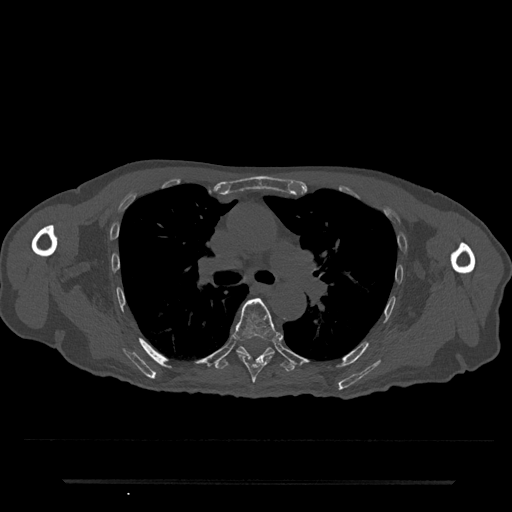
CT including the spine, one axial slice; position 513 of 797 along the scan axis; reconstruction kernel Br40s/3; 120 kVp; bone window (W 1800 / L 400 HU); 0.5 mm slice thickness; 512 × 512 image matrix. Patient: male, 74 years. Case-level facts recorded for this patient, not image findings: primary cancer: prostate.
Structures marked on this image (semi-automatically segmented with operator editing):
- T6 vertebra: bounding box (x1, y1, x2, y2) in pixels: (233, 298, 280, 383)
- T7 vertebra: (216, 346, 295, 371)